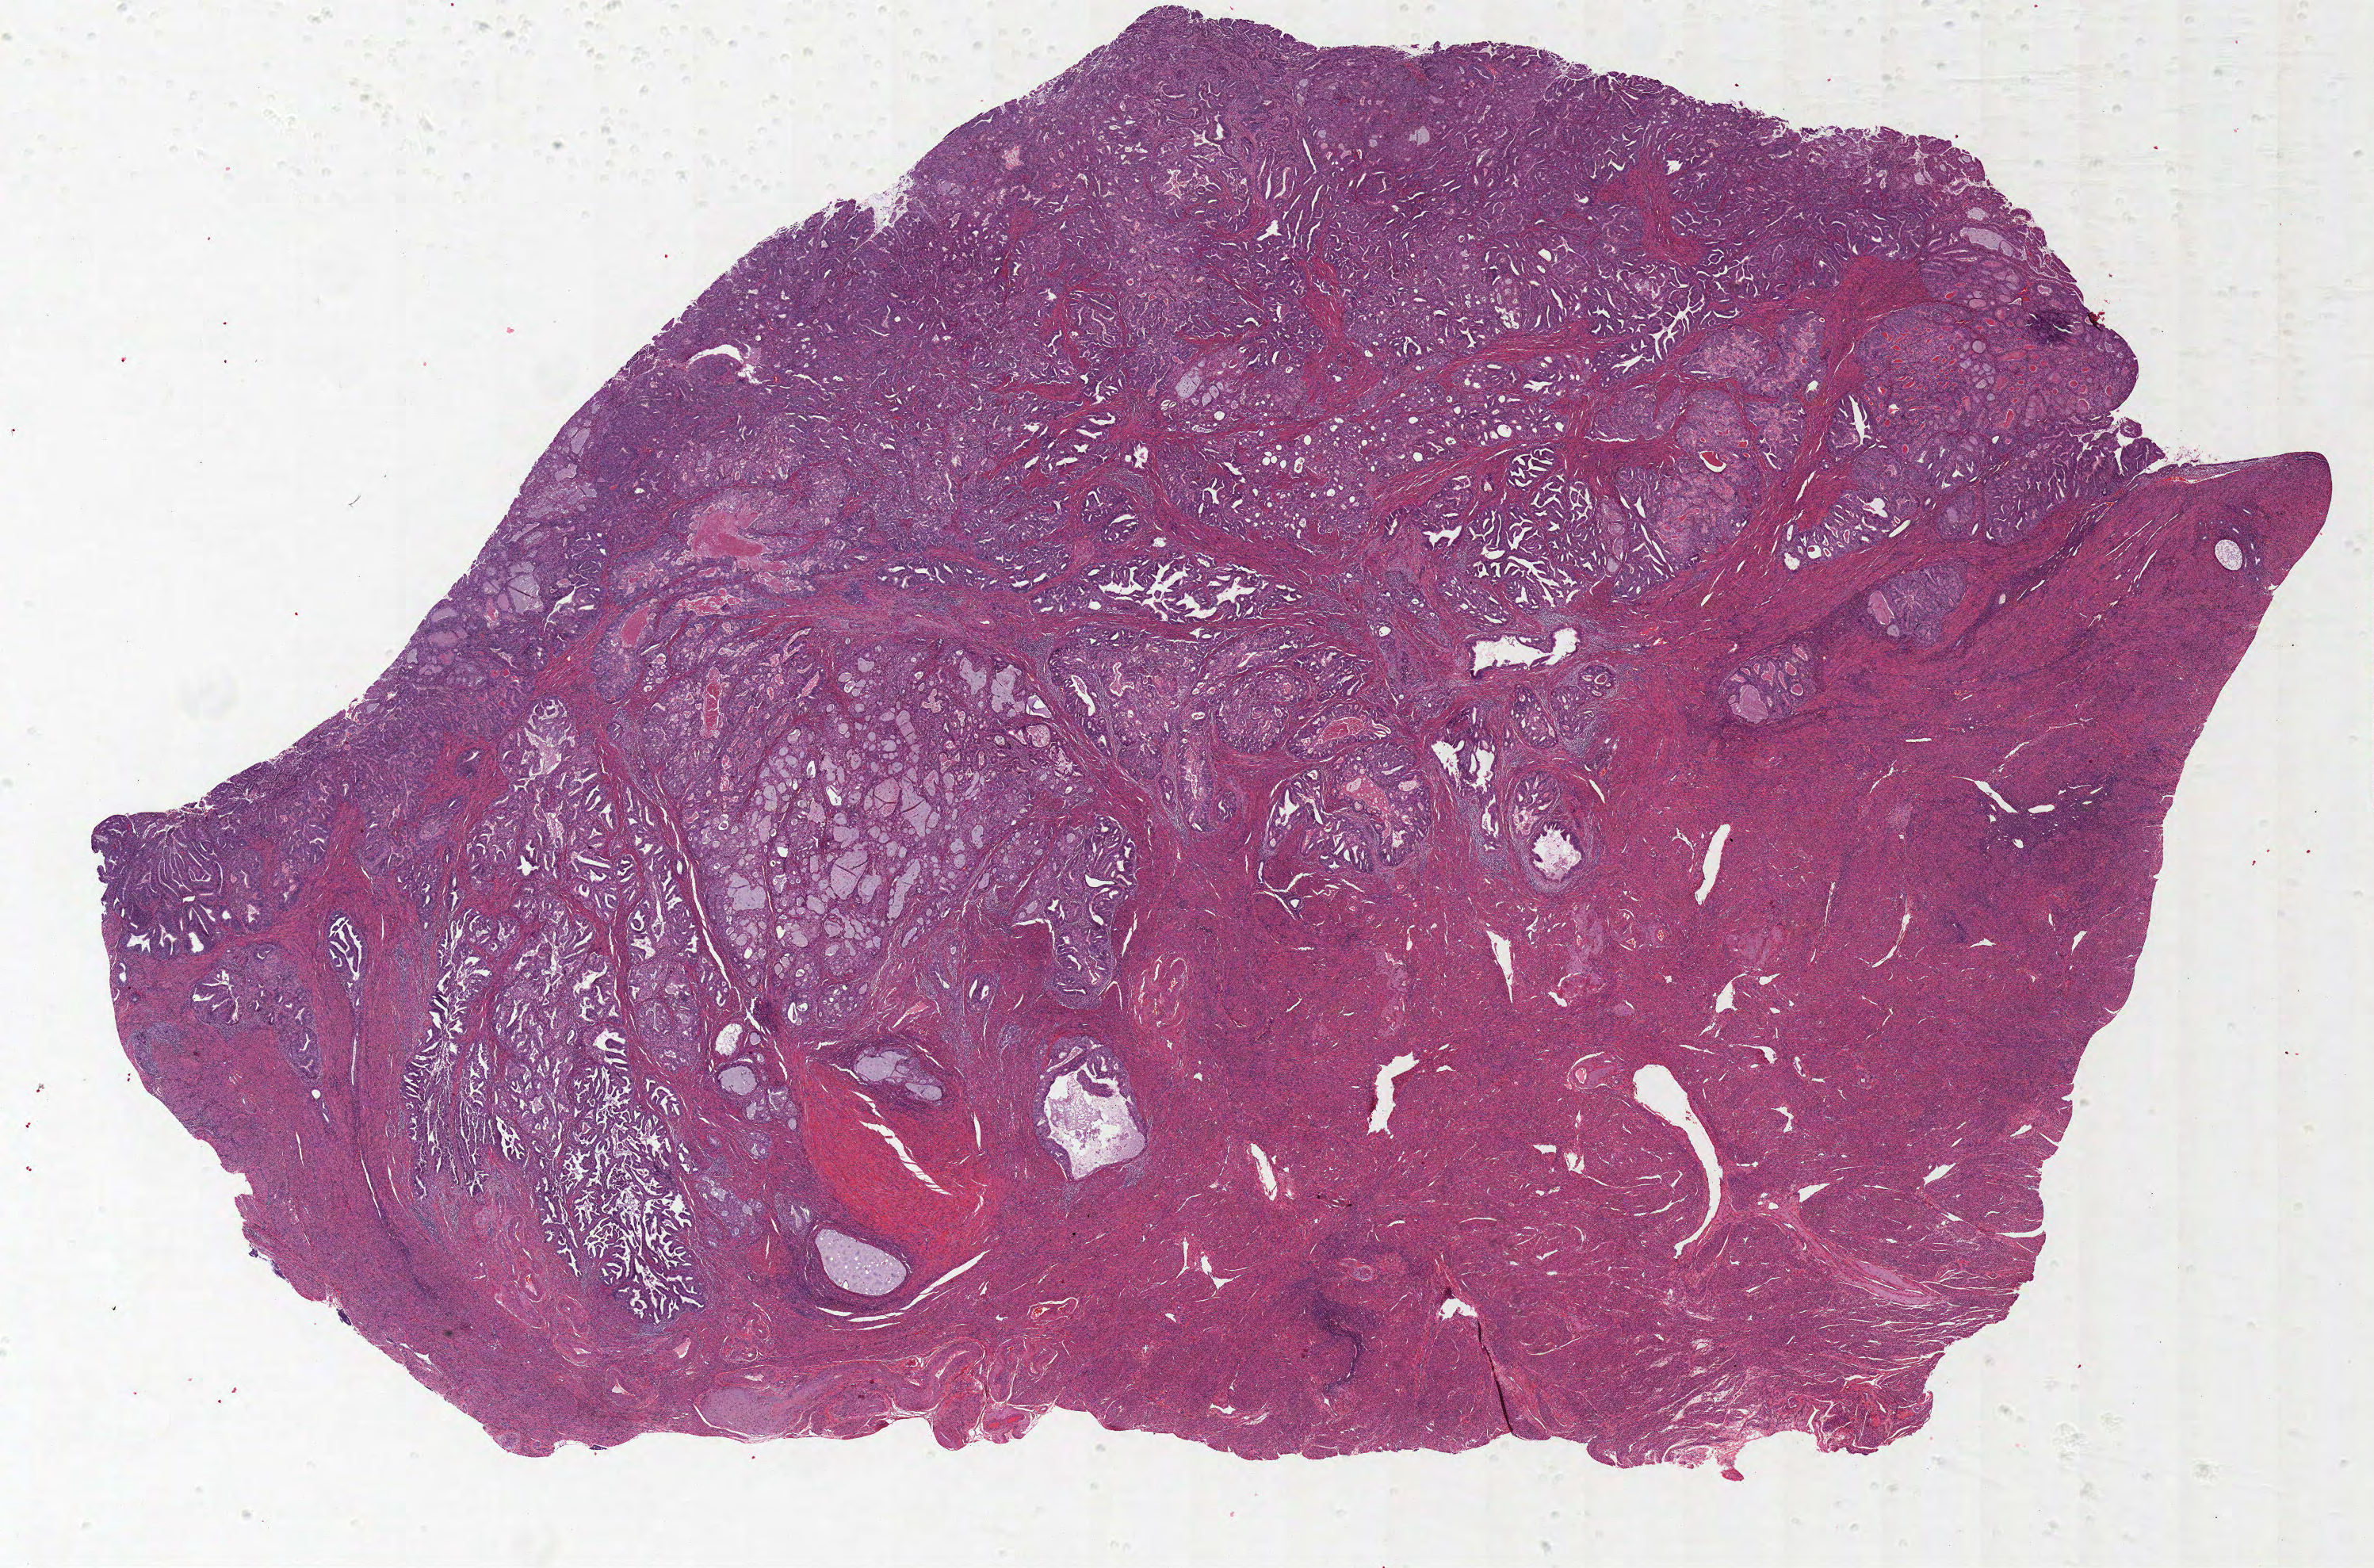
H&E whole-slide image — whole scanned area (about 23.9 x 15.8 mm) shown as a low-resolution overview; formalin-fixed paraffin-embedded (FFPE) diagnostic section; primary tumour sample from the uterus. Female, age 70 years at initial diagnosis. Histologic grade: G2 (moderately differentiated).
* FIGO stage: IA
* diagnosis: Serous cystadenocarcinoma, NOS (endometrium)